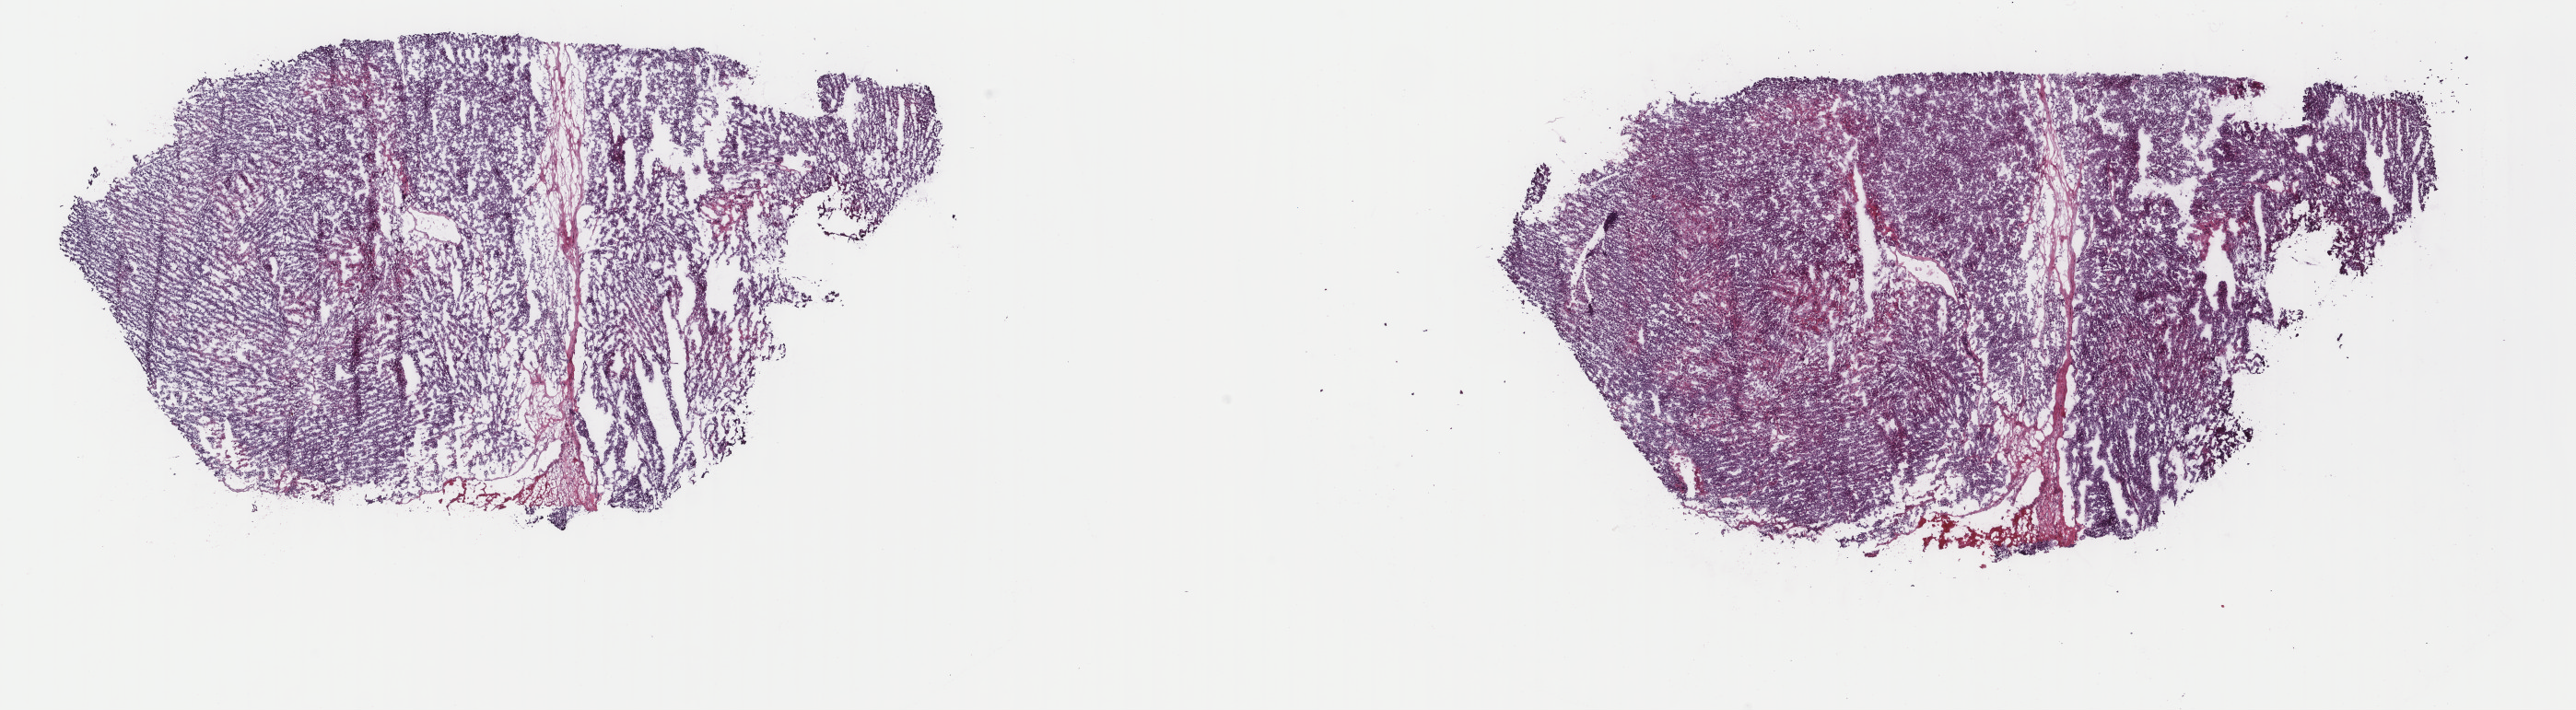
Whole-slide histology image, H&E — shown as a low-resolution overview of the whole scanned area (about 22.2 x 6.1 mm). Frozen section. Primary tumour sample from the adrenal cortex. Female patient; age at initial diagnosis 25 years. Composition of this section per pathologist review: tumour cells 99%, tumour nuclei 80%, normal cells 0%, stromal cells 0%, necrosis 1%. Inflammatory infiltration, as recorded: lymphocyte infiltration 1%, monocyte infiltration 0%, neutrophil infiltration 0%.
Diagnosis: Adrenal cortical carcinoma (cortex of adrenal gland).